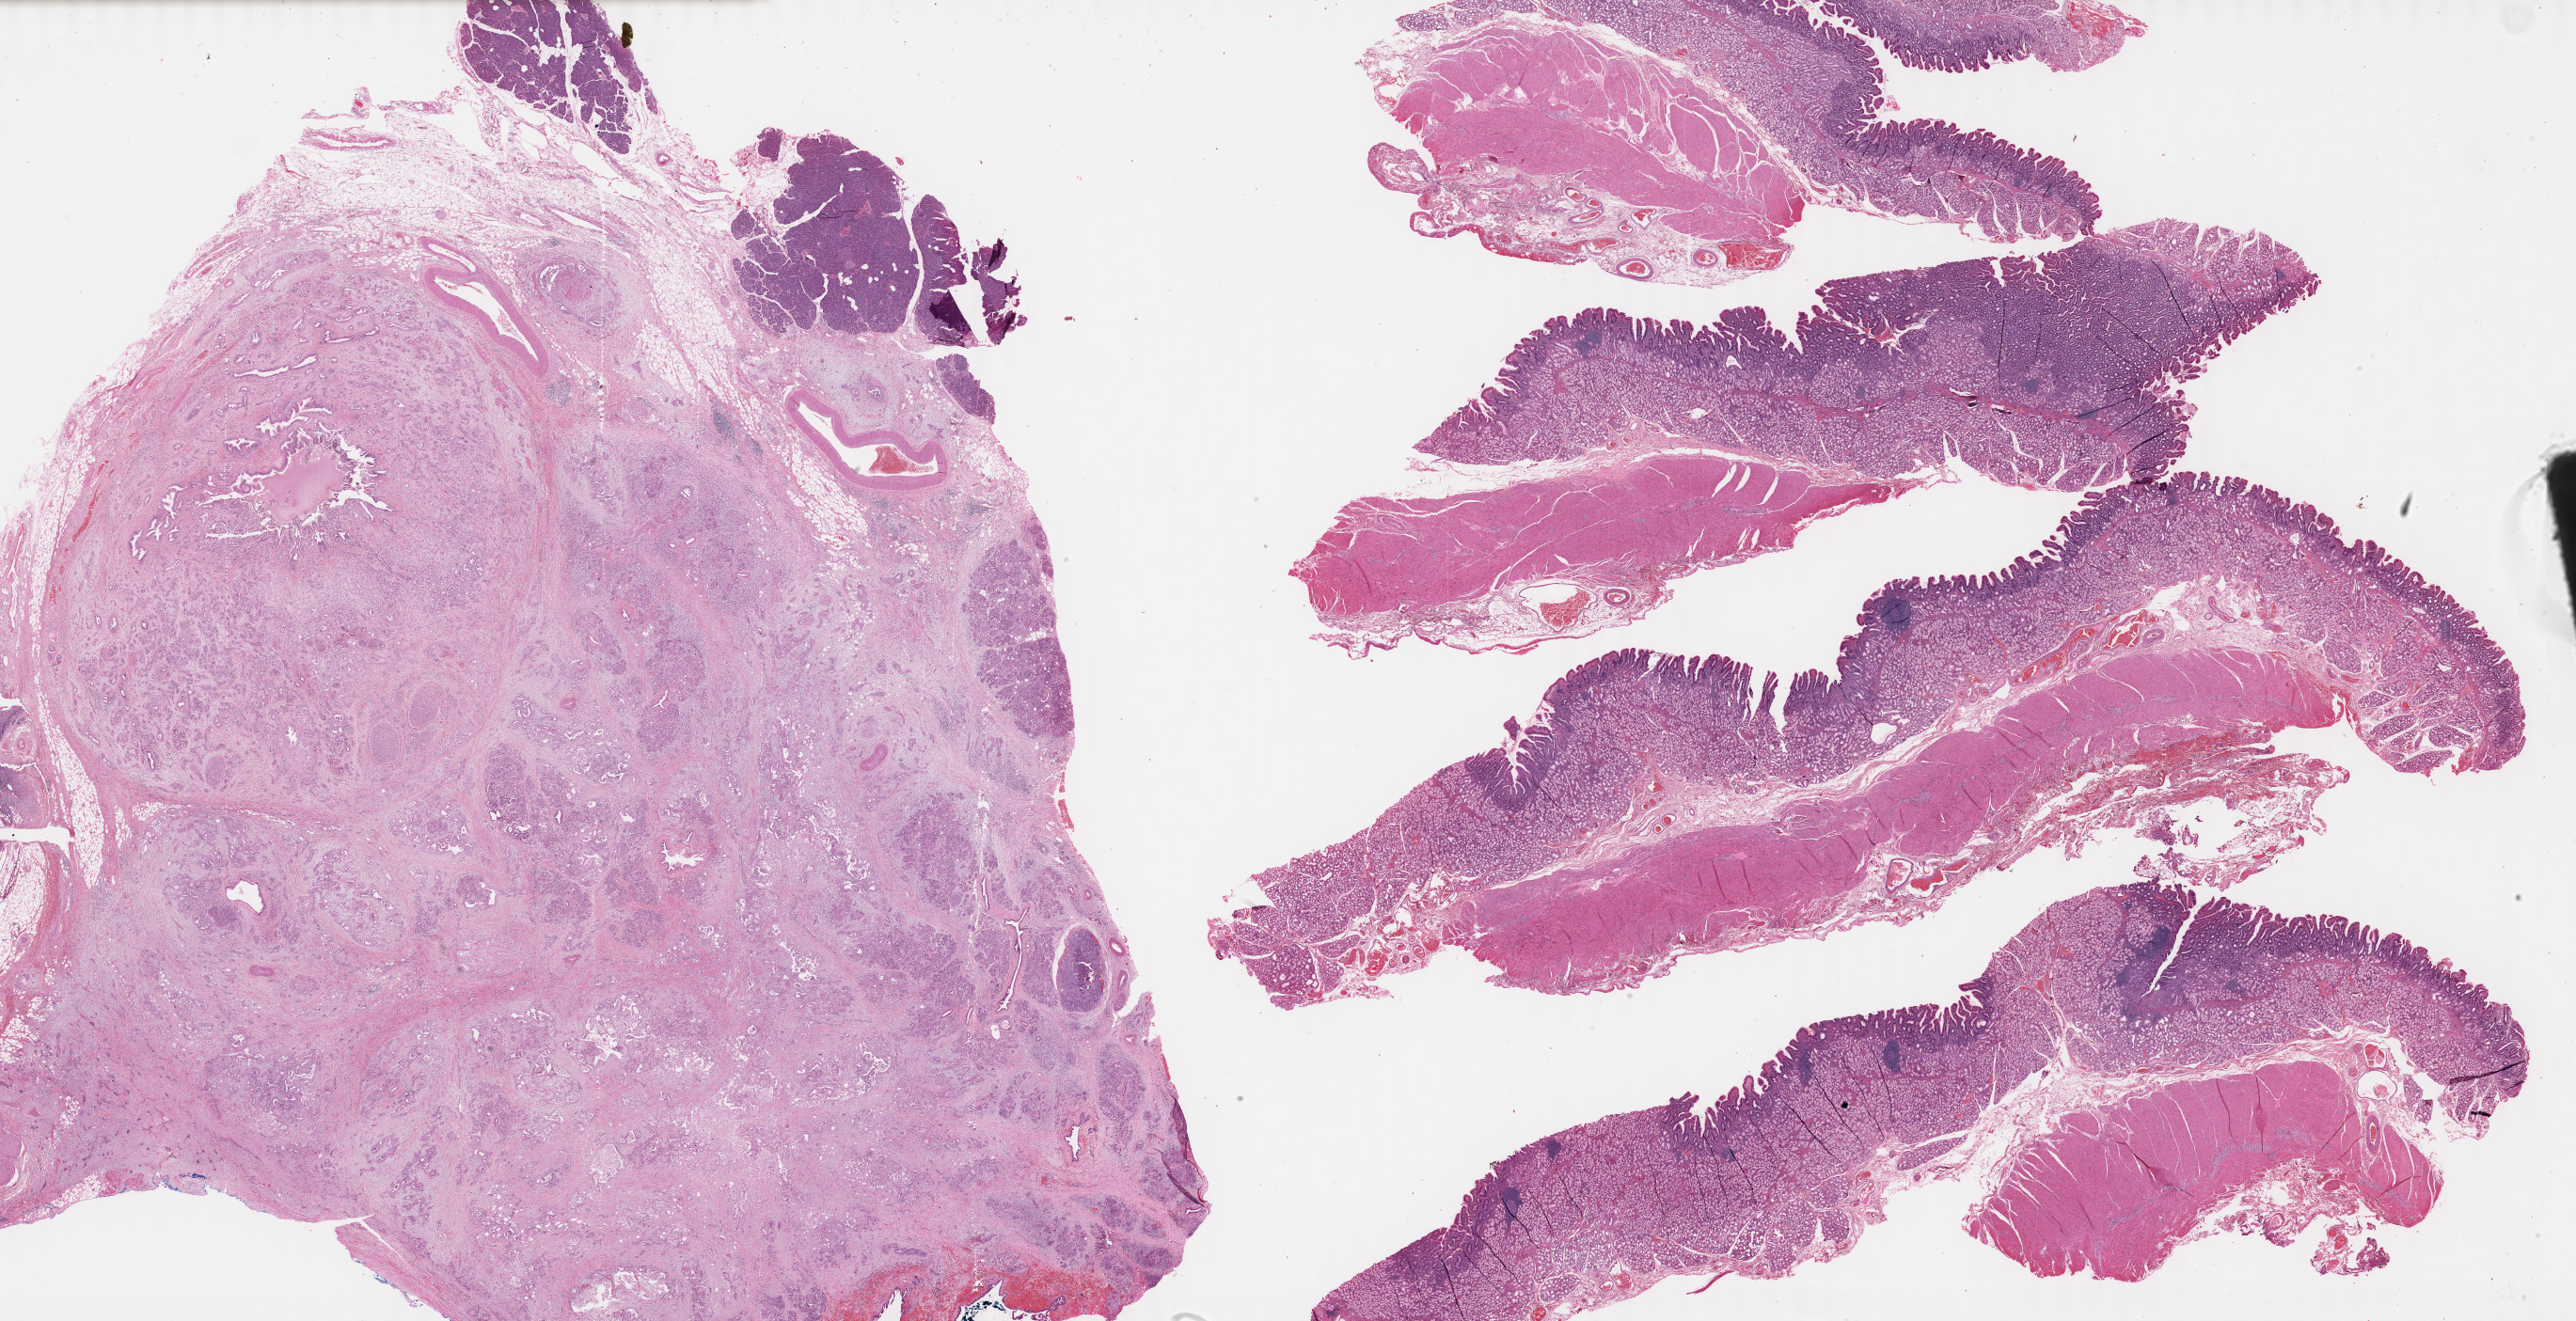
Whole-slide histology image, H&E-stained — low-resolution overview of the scanned area, about 44.3 x 22.7 mm (acquisition: 40x scan), formalin-fixed paraffin-embedded (FFPE) diagnostic section, primary tumour sample from the pancreas. Patient: male, age at initial diagnosis 67 years.
Pathologic diagnosis: Infiltrating duct carcinoma, NOS (head of pancreas).